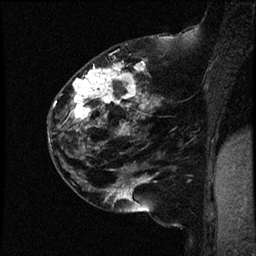
Breast MRI (dynamic contrast-enhanced), one sagittal slice. Slice 27 of 44 in the series (ordered by position). Dynamic contrast-enhanced study with each time point stored as its own series, time point 2 of 4 at this slice position (early post-contrast, ordered by acquisition time). 1.5 T. TE 4.2 ms, TR 17.7 ms. 256 × 256 image matrix, field of view 200 × 200 mm. Female patient, age 52 years. Case-level facts recorded for this patient, not image findings: setting: breast cancer imaged before/during neoadjuvant chemotherapy; receptor status: HR-positive, HER2-negative.
Annotated regions visible in this slice (semi-automatic segmentation, software-assisted and operator-edited):
- analysis volume of interest (the breast-tissue region the enhancement analysis was run in; not a lesion): bounding box <47,48,163,147> (left, top, right, bottom; pixels)
- tumour enhancement mask (voxels above the 100 % enhancement threshold inside the analysis volume of interest): <59,57,148,135>